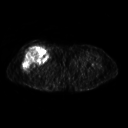
FDG PET of an extremity soft-tissue mass (from a PET/CT study), one axial slice. Slice 262 of 311 in the series (ordered by position). 3.27 mm slice thickness. 128 × 128 image matrix. Patient: female, 57 years. Case-level facts recorded for this patient, not image findings: histological type: pleiomorphic undifferentiated sarcoma; grade: high; site of the primary tumour: right quadricep.
Annotated regions visible in this slice (expert contour drawn on MRI and transferred to this co-registered scan by the dataset authors):
- tumour plus oedema (research contour): bounding box (x1, y1, x2, y2) in pixels: (22, 46, 48, 71)
- tumour (research contour): (22, 46, 48, 71)